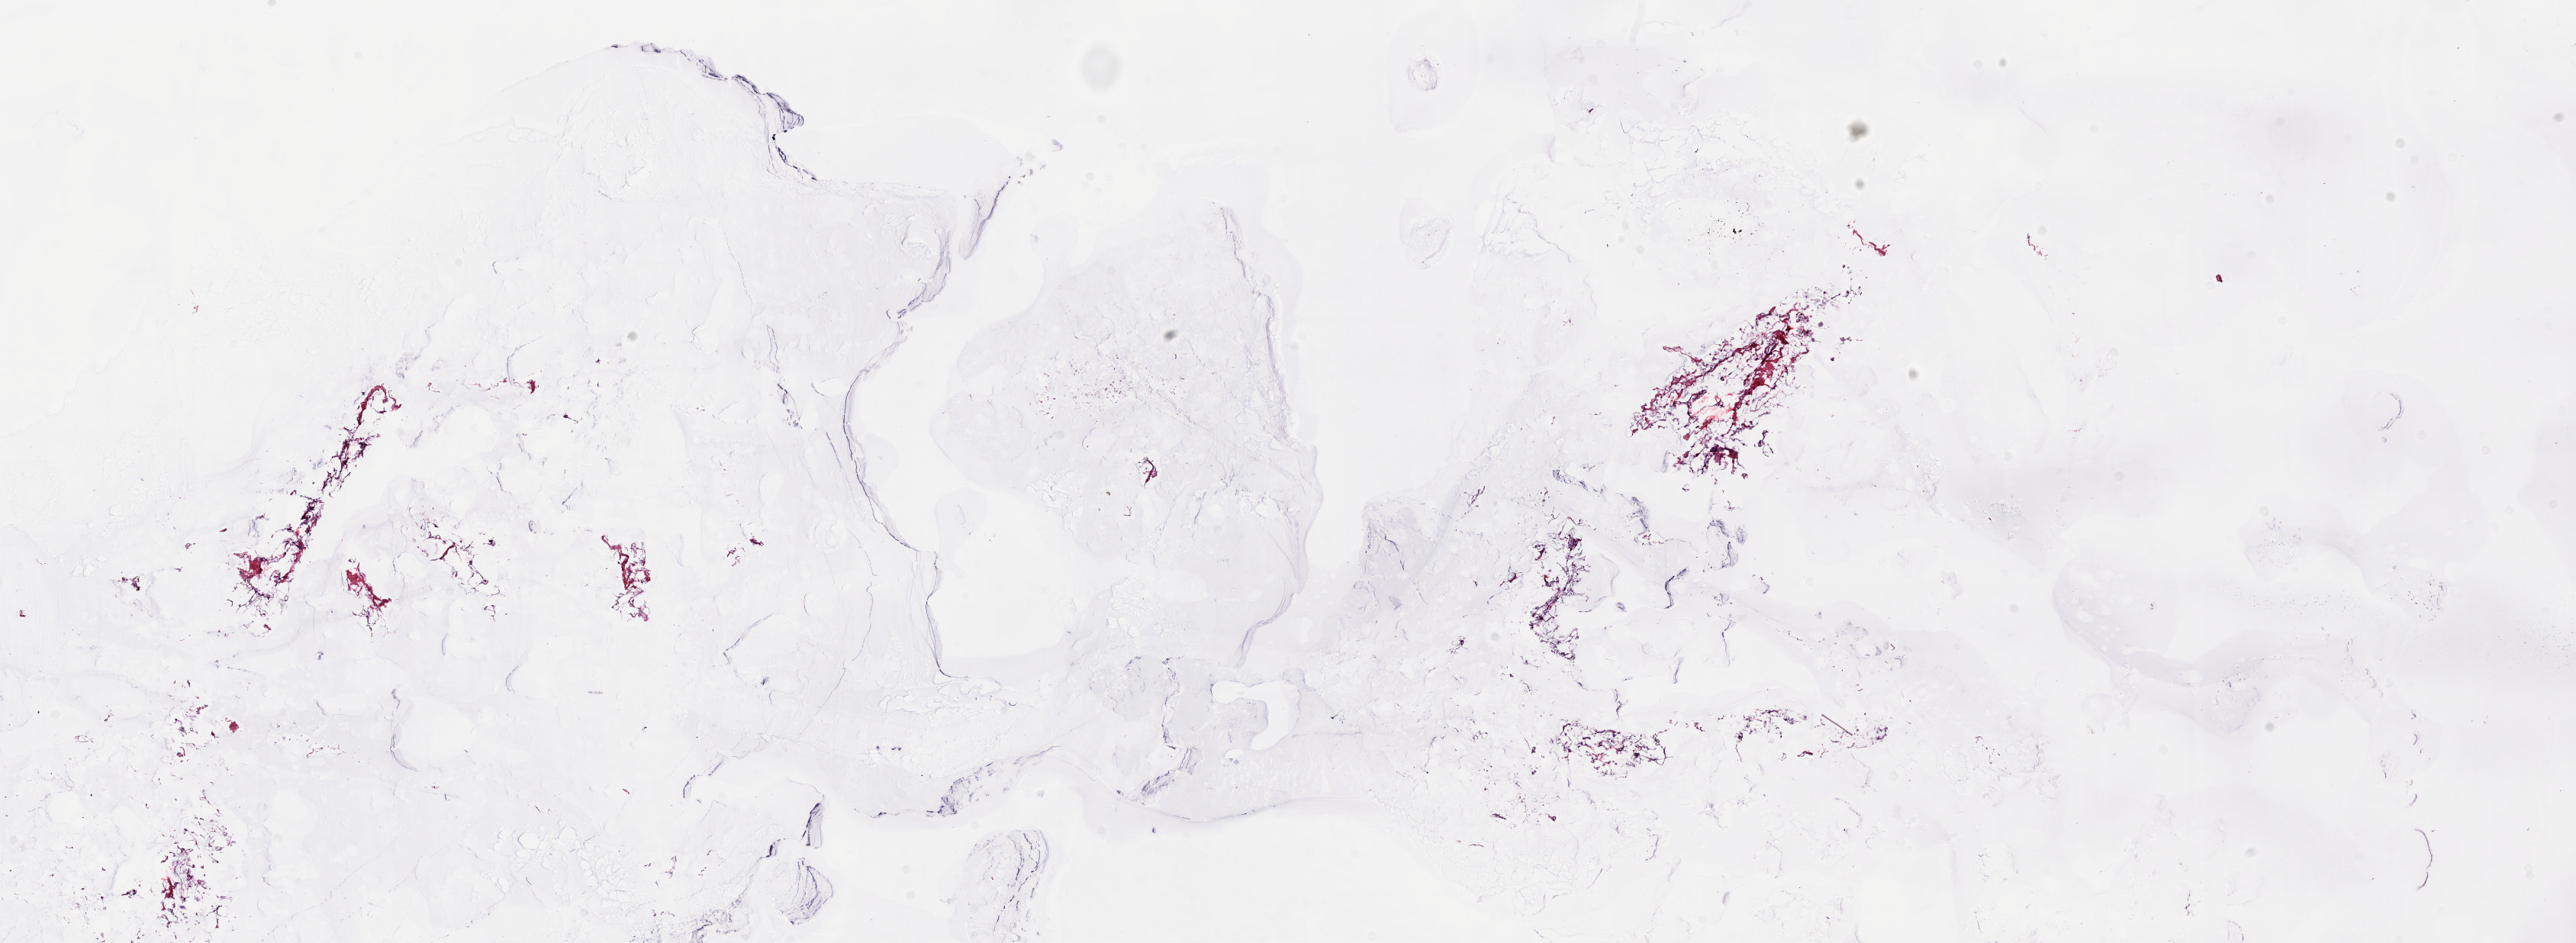
H&E-stained whole-slide image — low-resolution overview of the scanned area, about 26.8 x 9.8 mm (acquisition: 20x scan), frozen section, sample: solid tissue normal (non-tumour tissue), breast. Patient: female, age at initial diagnosis 84 years. Pathologist review of this section (percent, as recorded): tumour cells 0%, tumour nuclei 0%.
This section: solid tissue normal sample (biorepository sample class). Patient diagnosis: Infiltrating duct carcinoma, NOS.